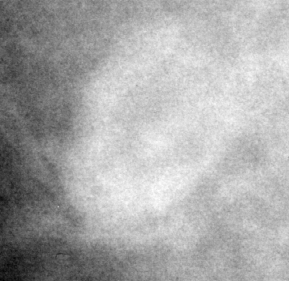
Crop from a digitized film mammogram around one marked abnormality, right breast, MLO view.
Finding: mass, shape oval / lymph node, margins circumscribed; BI-RADS assessment category 2; subtlety rating 4 on a 1 (subtle) to 5 (obvious) scale; benign without callback (not worked up further).